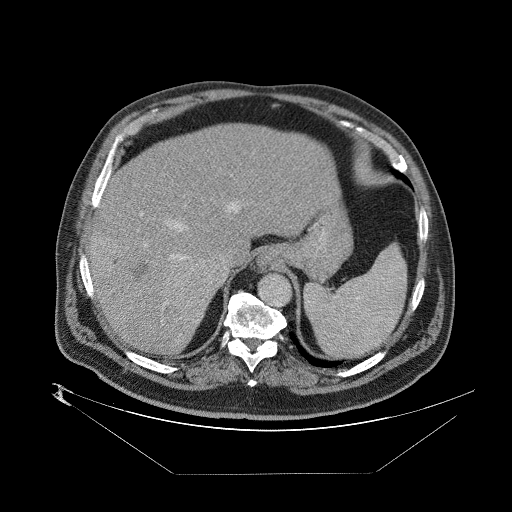
Contrast-enhanced abdominal CT (liver protocol), one axial slice; position 62 of 89 along the scan axis; one of 2 acquisitions stored at this slice position; soft-tissue window (W 400 / L 40 HU); 512 × 512 image matrix, field of view 480 × 480 mm. Case-level facts recorded for this patient, not image findings: diagnosis: hepatocellular carcinoma (patient treated with transarterial chemoembolisation; whether this scan precedes or follows treatment is not stated here); TNM stage (as recorded): Stage-II; Child-Pugh class: B; tumour differentiation: moderately differentiated; tumour nodularity: multinodular.
Structures marked on this image (semi-automatically segmented with operator editing):
- abdominal aorta: bounding box <258,274,292,307> (left, top, right, bottom; pixels)
- liver parenchyma outside the tumour (the mass and vessels are separate outlines, so this box may not span the whole liver): <90,120,344,354>
- mass: <87,234,227,324>
- liver vessels: <96,198,330,304>